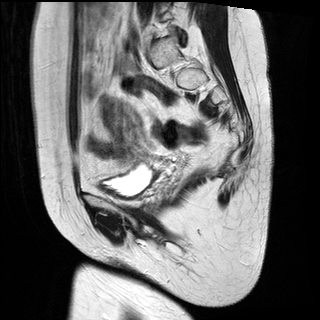
Pelvic MRI for cervical cancer, one sagittal slice; slice 18 of 28 in the series (ordered by position); T2-weighted; 1.5 T; TE 89 ms, TR 2740 ms; 4 mm slice thickness; 320 × 320 image matrix. Patient: female, 49 years.
Outlined on this slice (manually delineated by an expert):
- uterus and cervix: box from (x=98, y=93) to (x=134, y=150) px